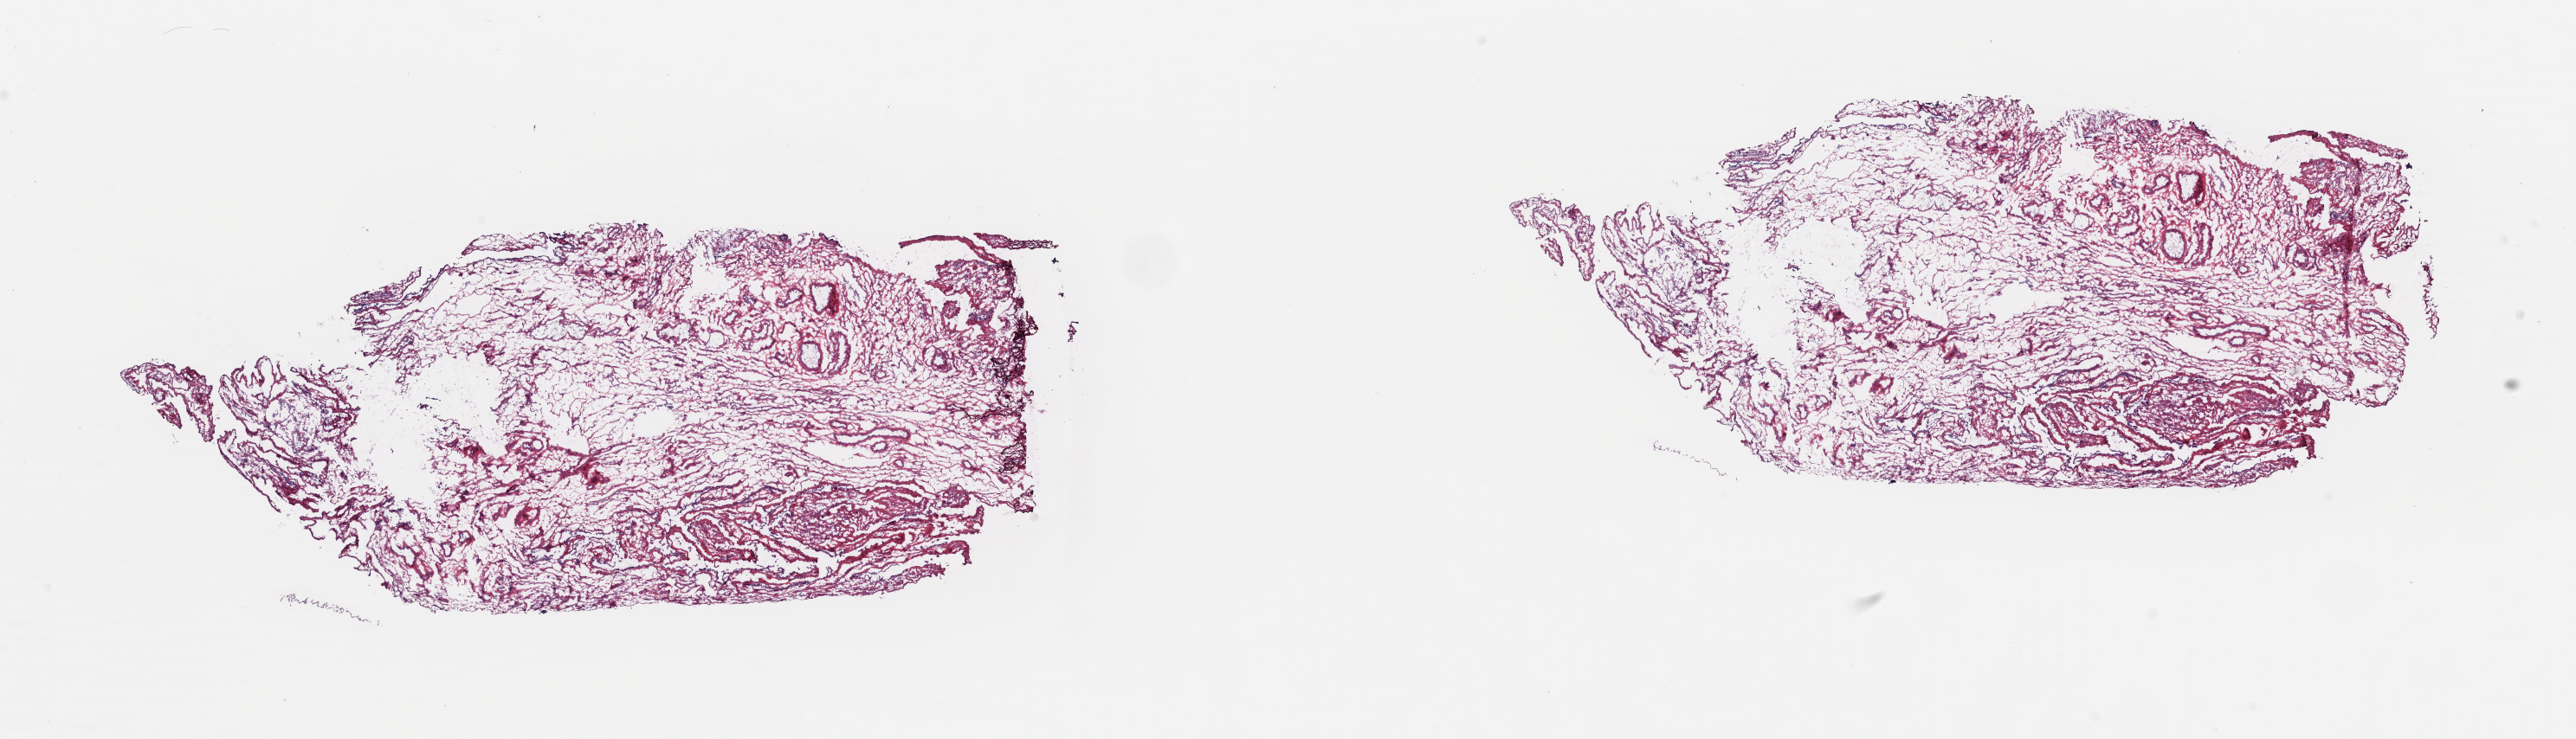
Digitized Hematoxylin and eosin (H&E) stained tissue section (whole slide), whole scanned area (about 23.5 x 6.7 mm, from a 40x scan) shown as a low-resolution overview; frozen section; solid tissue normal (non-tumour tissue) sample from the cervix. Female, age 51 years at initial diagnosis. Slide review estimates, as recorded: normal cells 100%.
This section: solid tissue normal (non-tumour) sample from the same patient. Patient diagnosis: Squamous cell carcinoma, keratinizing, NOS (cervix uteri).